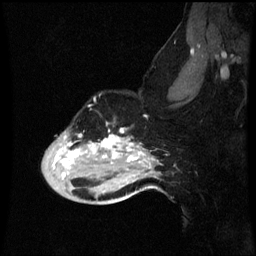
Breast MRI (dynamic contrast-enhanced), one sagittal slice; slice 45 of 60 in the series (ordered by position); dynamic contrast-enhanced series, image 2 of 3 at this slice position (ordered by acquisition); 1.5 T; TE 4.2 ms, TR 8.9 ms; 2 mm slice thickness; 256 × 256 image matrix, field of view 200 × 200 mm. Patient: female, 49 years. Case-level facts recorded for this patient, not image findings: setting: breast cancer imaged before/during neoadjuvant chemotherapy; receptor status: HR-positive, HER2-negative.
Outlined on this slice (semi-automatic segmentation, software-assisted and operator-edited):
- analysis volume of interest (the breast-tissue region the enhancement analysis was run in; not a lesion): box from (x=42, y=126) to (x=159, y=199) px
- tumour enhancement mask (voxels above the 70 % enhancement threshold inside the analysis volume of interest): (x=56, y=130)–(x=155, y=179)